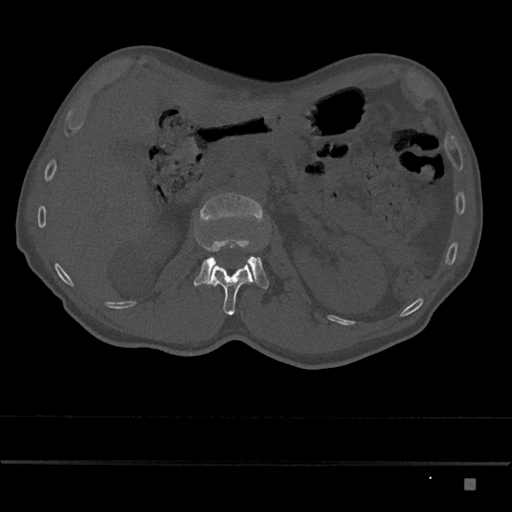
CT including the spine, one axial slice. Reconstruction kernel Br40s/3. 120 kVp. Bone window (W 1800 / L 400 HU). 512 × 512 image matrix, field of view 390 × 390 mm. Patient: male, 72 years. Case-level facts recorded for this patient, not image findings: primary cancer: prostate.
Outlined on this slice (semi-automatically segmented with operator editing):
- L1 vertebra: bounding box <208,262,255,315> (left, top, right, bottom; pixels)
- L2 vertebra: <194,193,269,289>